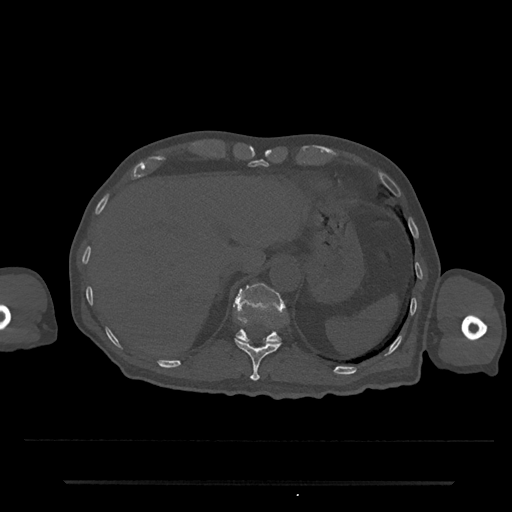
CT including the spine, one axial slice; position 233 of 797 along the scan axis; reconstruction kernel Br40s/3; bone window (W 1800 / L 400 HU); 0.5 mm slice thickness; 512 × 512 image matrix, field of view 427 × 427 mm. Patient: male, 74 years. Case-level facts recorded for this patient, not image findings: primary cancer: prostate.
Outlined on this slice (semi-automatic segmentation, software-assisted and operator-edited):
- T11 vertebra: bounding box (x1, y1, x2, y2) in pixels: (234, 338, 282, 381)
- T12 vertebra: (235, 283, 283, 344)